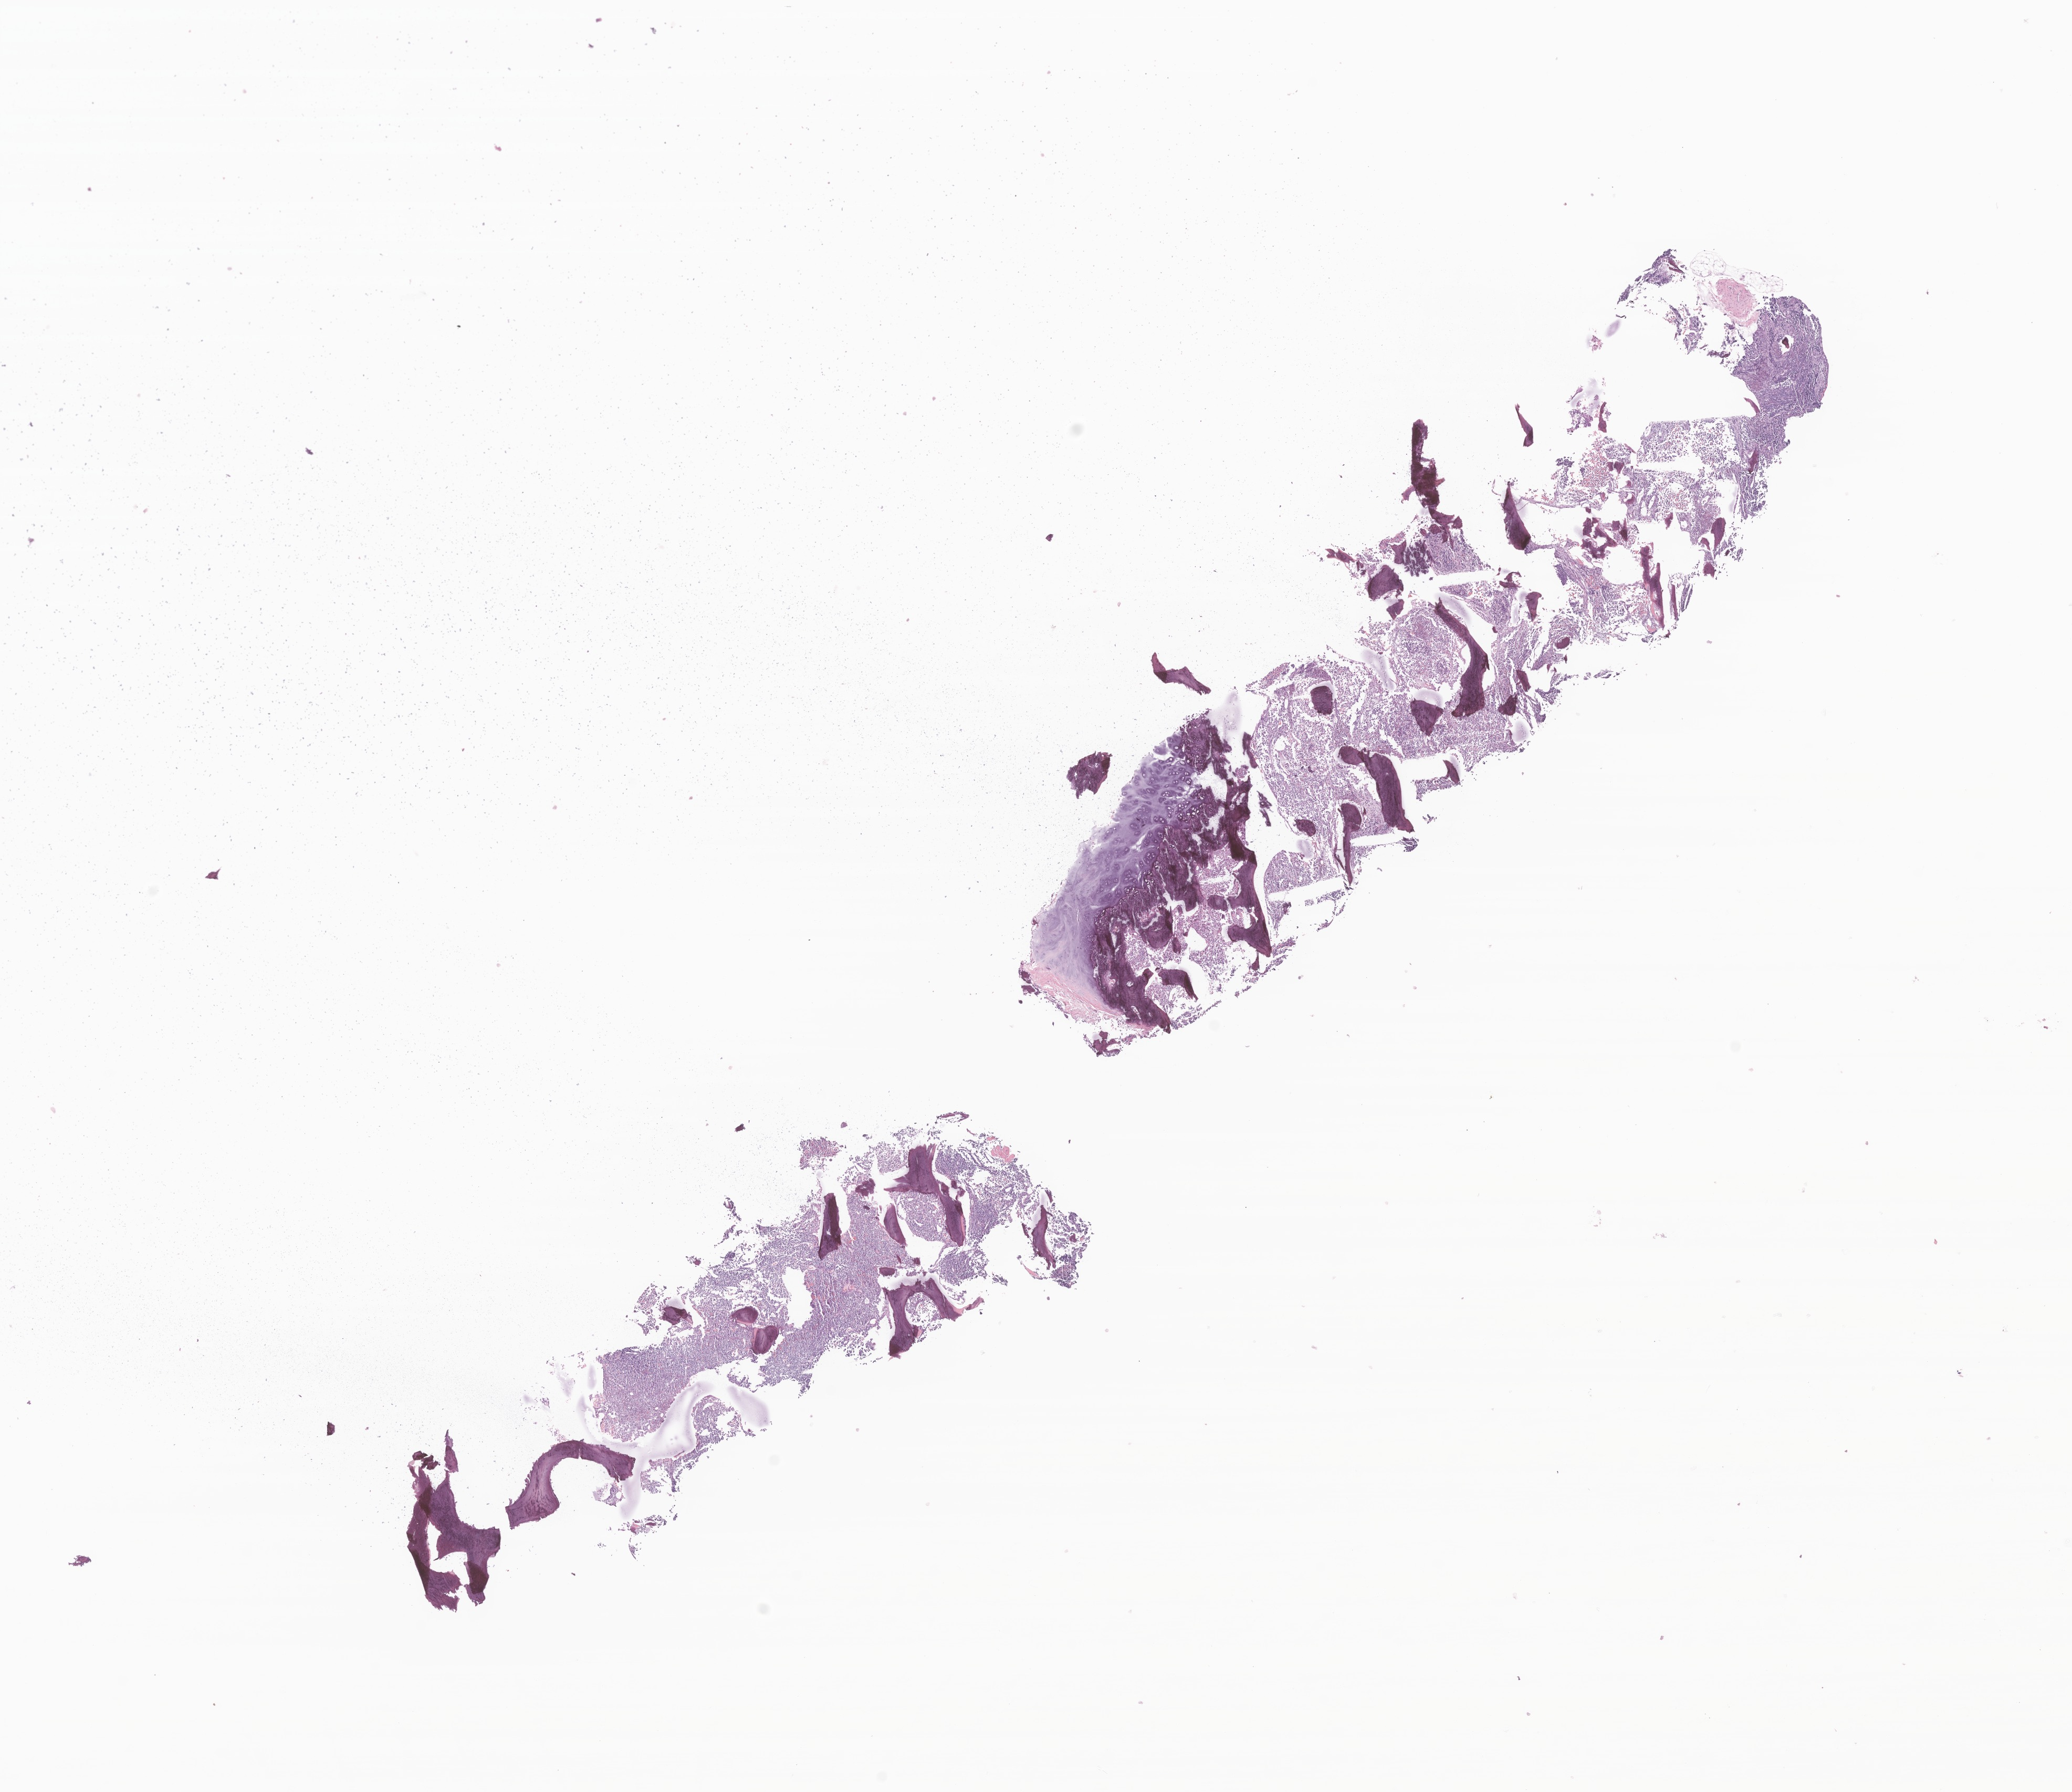
Digitized haematoxylin and eosin-stained section of tumor tissue — whole scanned area (about 16.6 x 14.4 mm) shown as a low-resolution overview, formalin-fixed paraffin-embedded section. Male patient, age 124 months (10 years 4 months).
Diagnosis: Rhabdomyosarcoma, NOS.